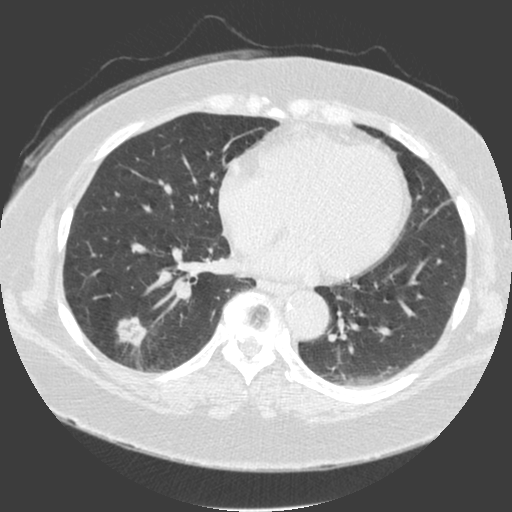
Low-dose screening chest CT, axial slice; third screening round (two years after baseline); lung window (W 1500 / L -600 HU); 2 mm slice thickness; 120 kVp. Female, age 56 years at enrolment. Current smoker at enrolment.
Lesion marked by an expert reader, bounding box [x1, y1, x2, y2] px = [100, 302, 156, 356]. The screening reader recorded 4 non-calcified nodules or masses ≥4 mm on this exam; which of them this box marks is not recorded. Official screen result: positive, other. Later outcome: lung cancer diagnosed 20 days after this screen — adenosquamous carcinoma, right lower lobe, poorly differentiated (G3), stage IA (AJCC 6th edition), 25 mm at pathology.